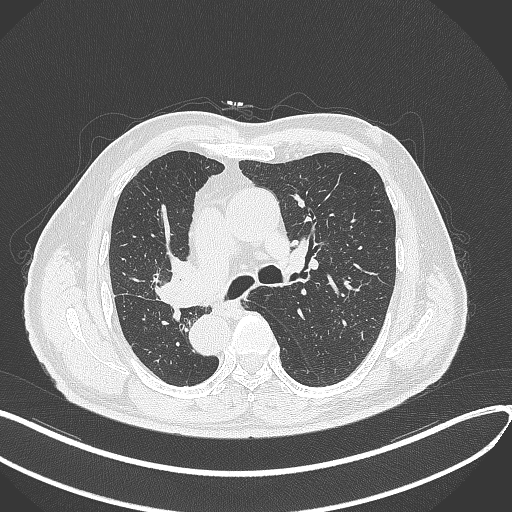
Chest CT, one axial slice; position 184 of 300 along the scan axis; reconstruction kernel B70f; 120 kVp; lung window (W 1500 / L -600 HU); 512 × 512 image matrix, field of view 400 × 400 mm. Male patient, age 67 years. Case-level facts recorded for this patient, not image findings: clinical TNM (as recorded): T2a N0 M0.
Annotated regions visible in this slice (bounding box drawn by a radiologist):
- lung tumour (recorded histology: squamous cell carcinoma): bounding box [x1, y1, x2, y2] px = [149, 249, 204, 312]